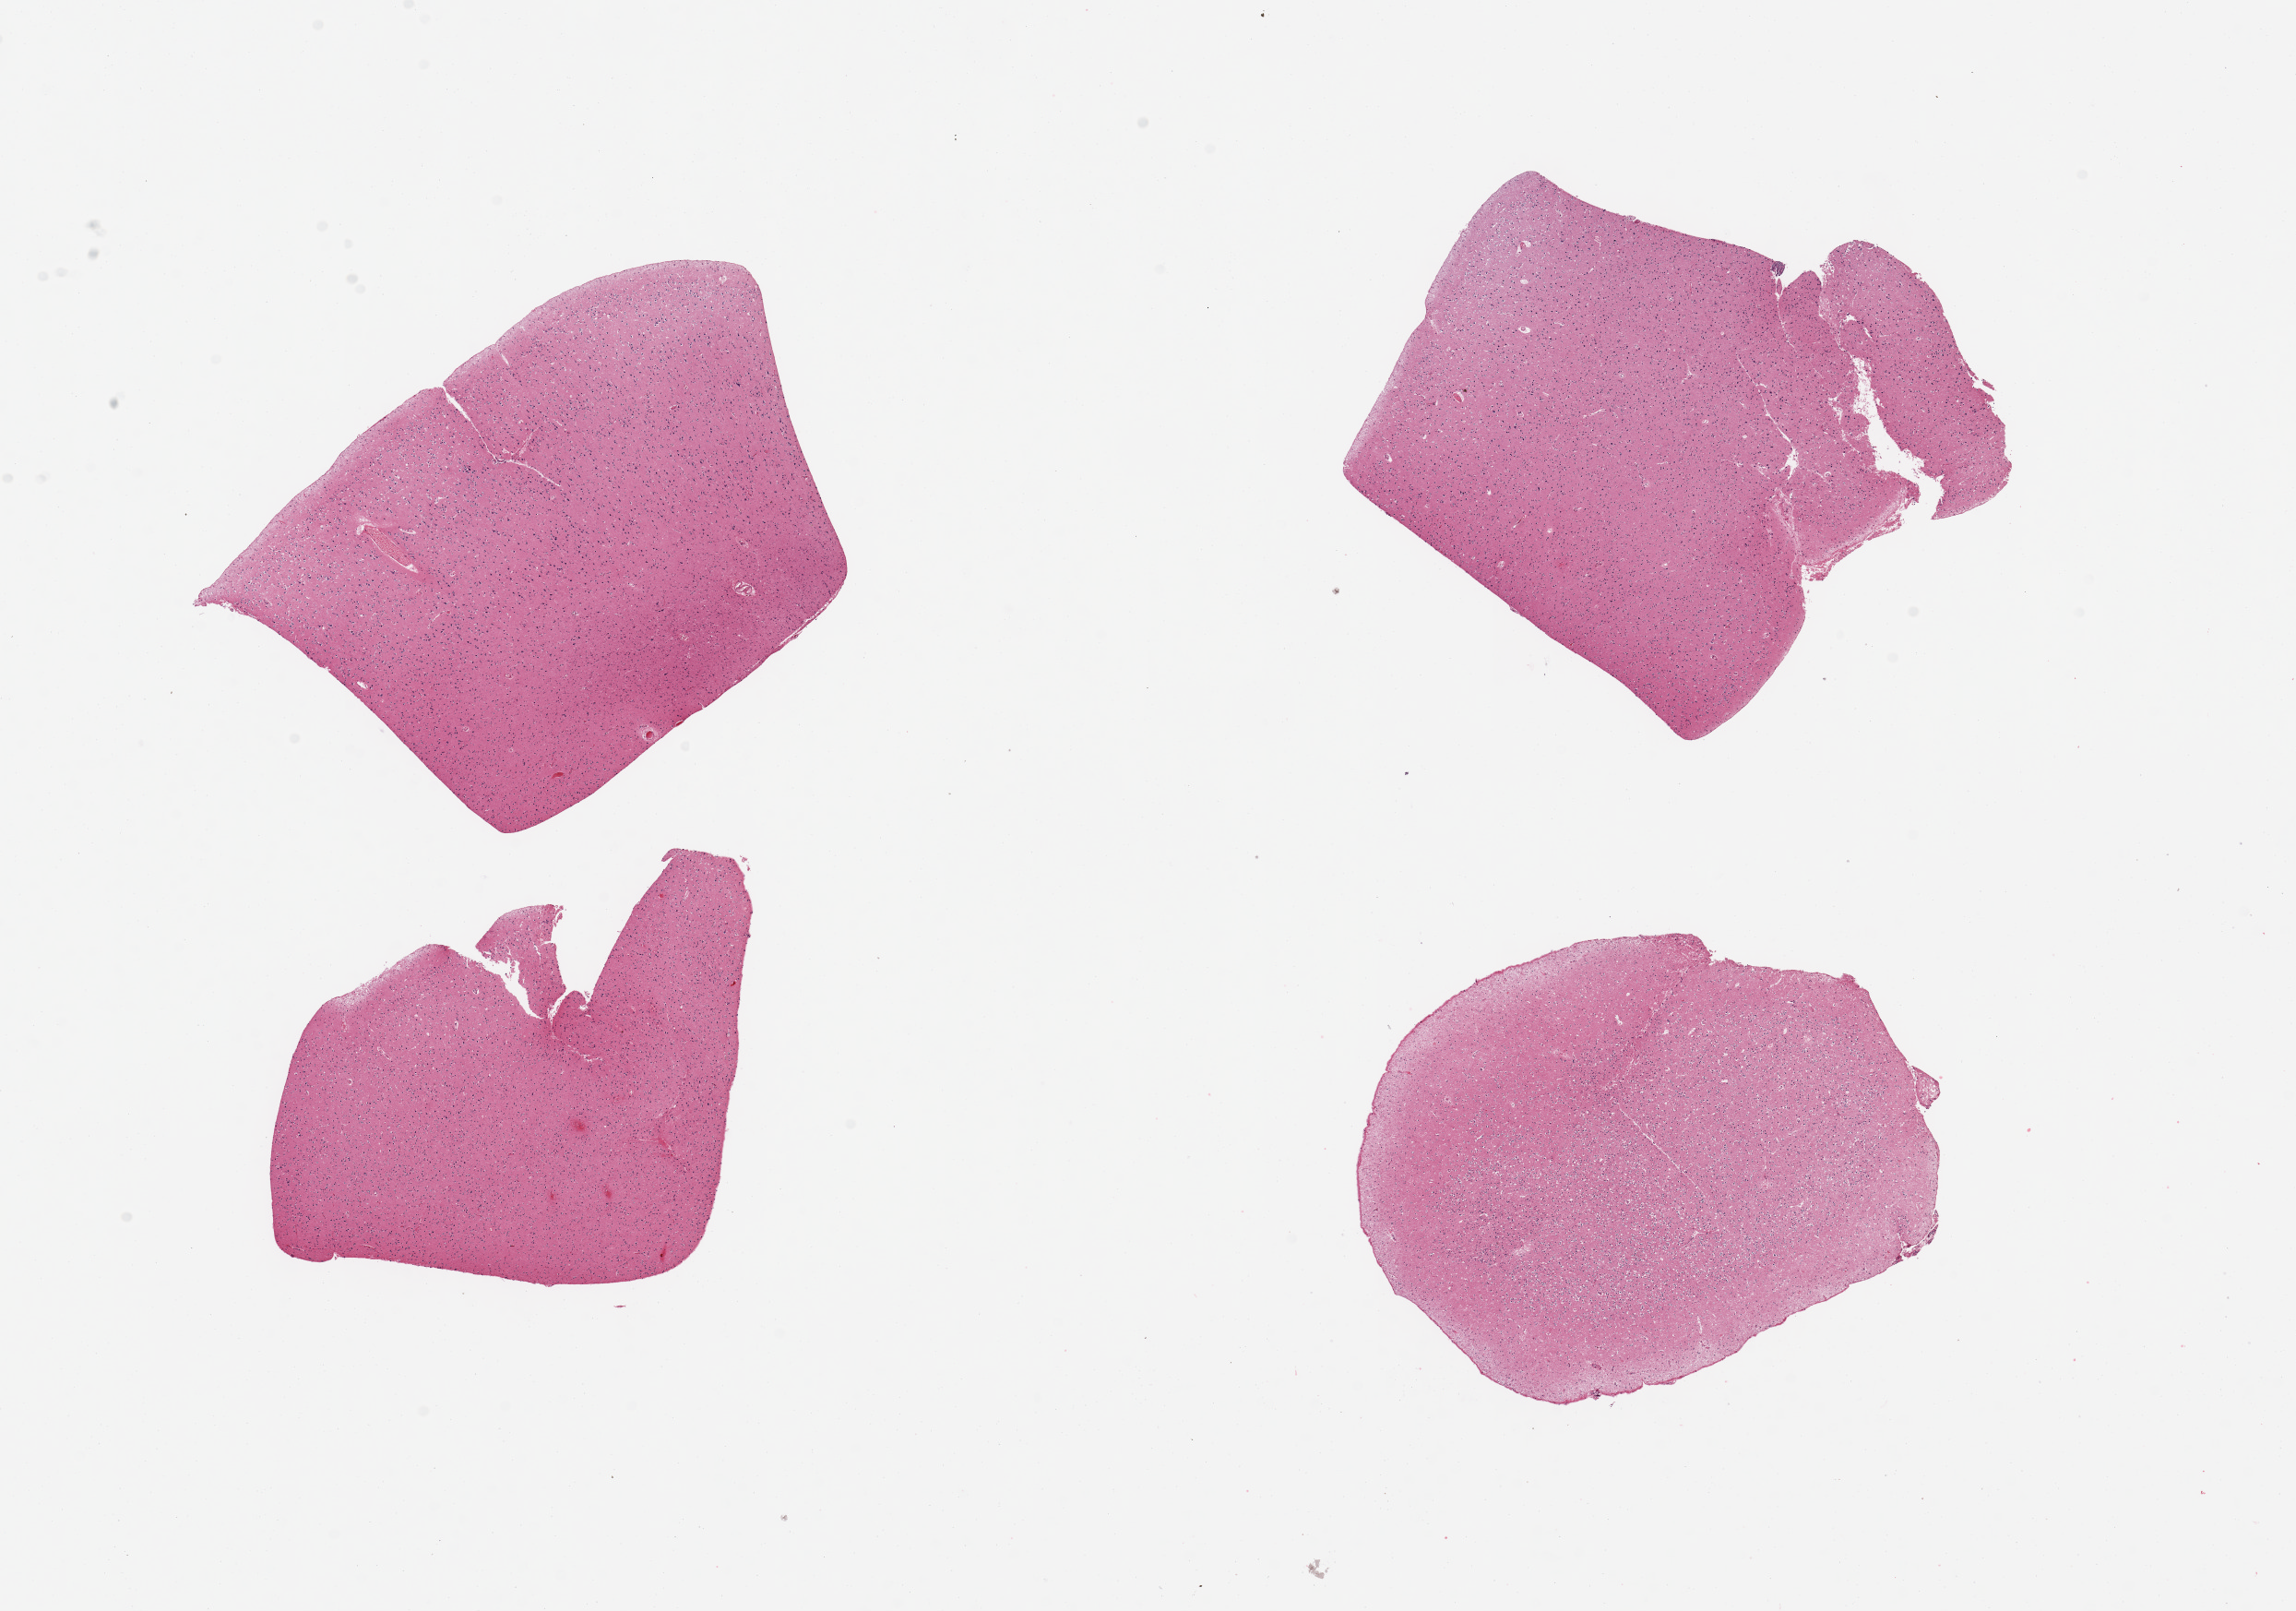
Whole-slide image, H&E stain, whole scanned area (about 19.7 x 13.8 mm, from a 20x scan) shown as a low-resolution overview. PAXgene-fixed, paraffin-embedded tissue. Target tissue: cerebral cortex. Tissue donor sample. Donor: male.
Pathologist's review note for this sample: 4 pieces.